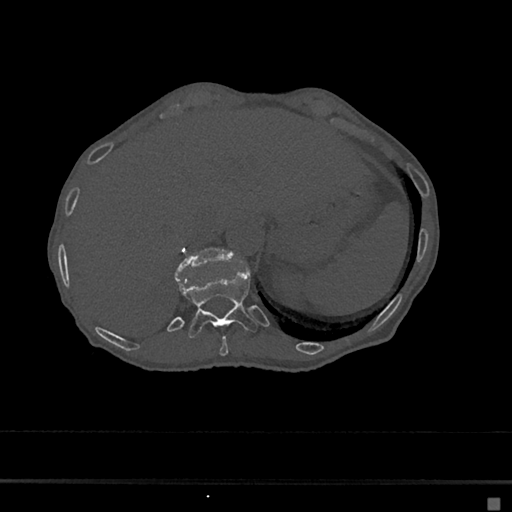
CT including the spine, one axial slice; position 175 of 797 along the scan axis; reconstruction kernel Br40s/3; bone window (W 1800 / L 400 HU); 0.5 mm slice thickness; 512 × 512 image matrix, field of view 360 × 360 mm. Patient: female, 68 years. From the clinical record (not read from this slice): primary cancer: renal.
Annotated regions visible in this slice (semi-automatically segmented with operator editing):
- T10 vertebra: bounding box <219,336,228,357> (left, top, right, bottom; pixels)
- T11 vertebra: <175,270,257,339>
- T12 vertebra: <175,247,233,275>